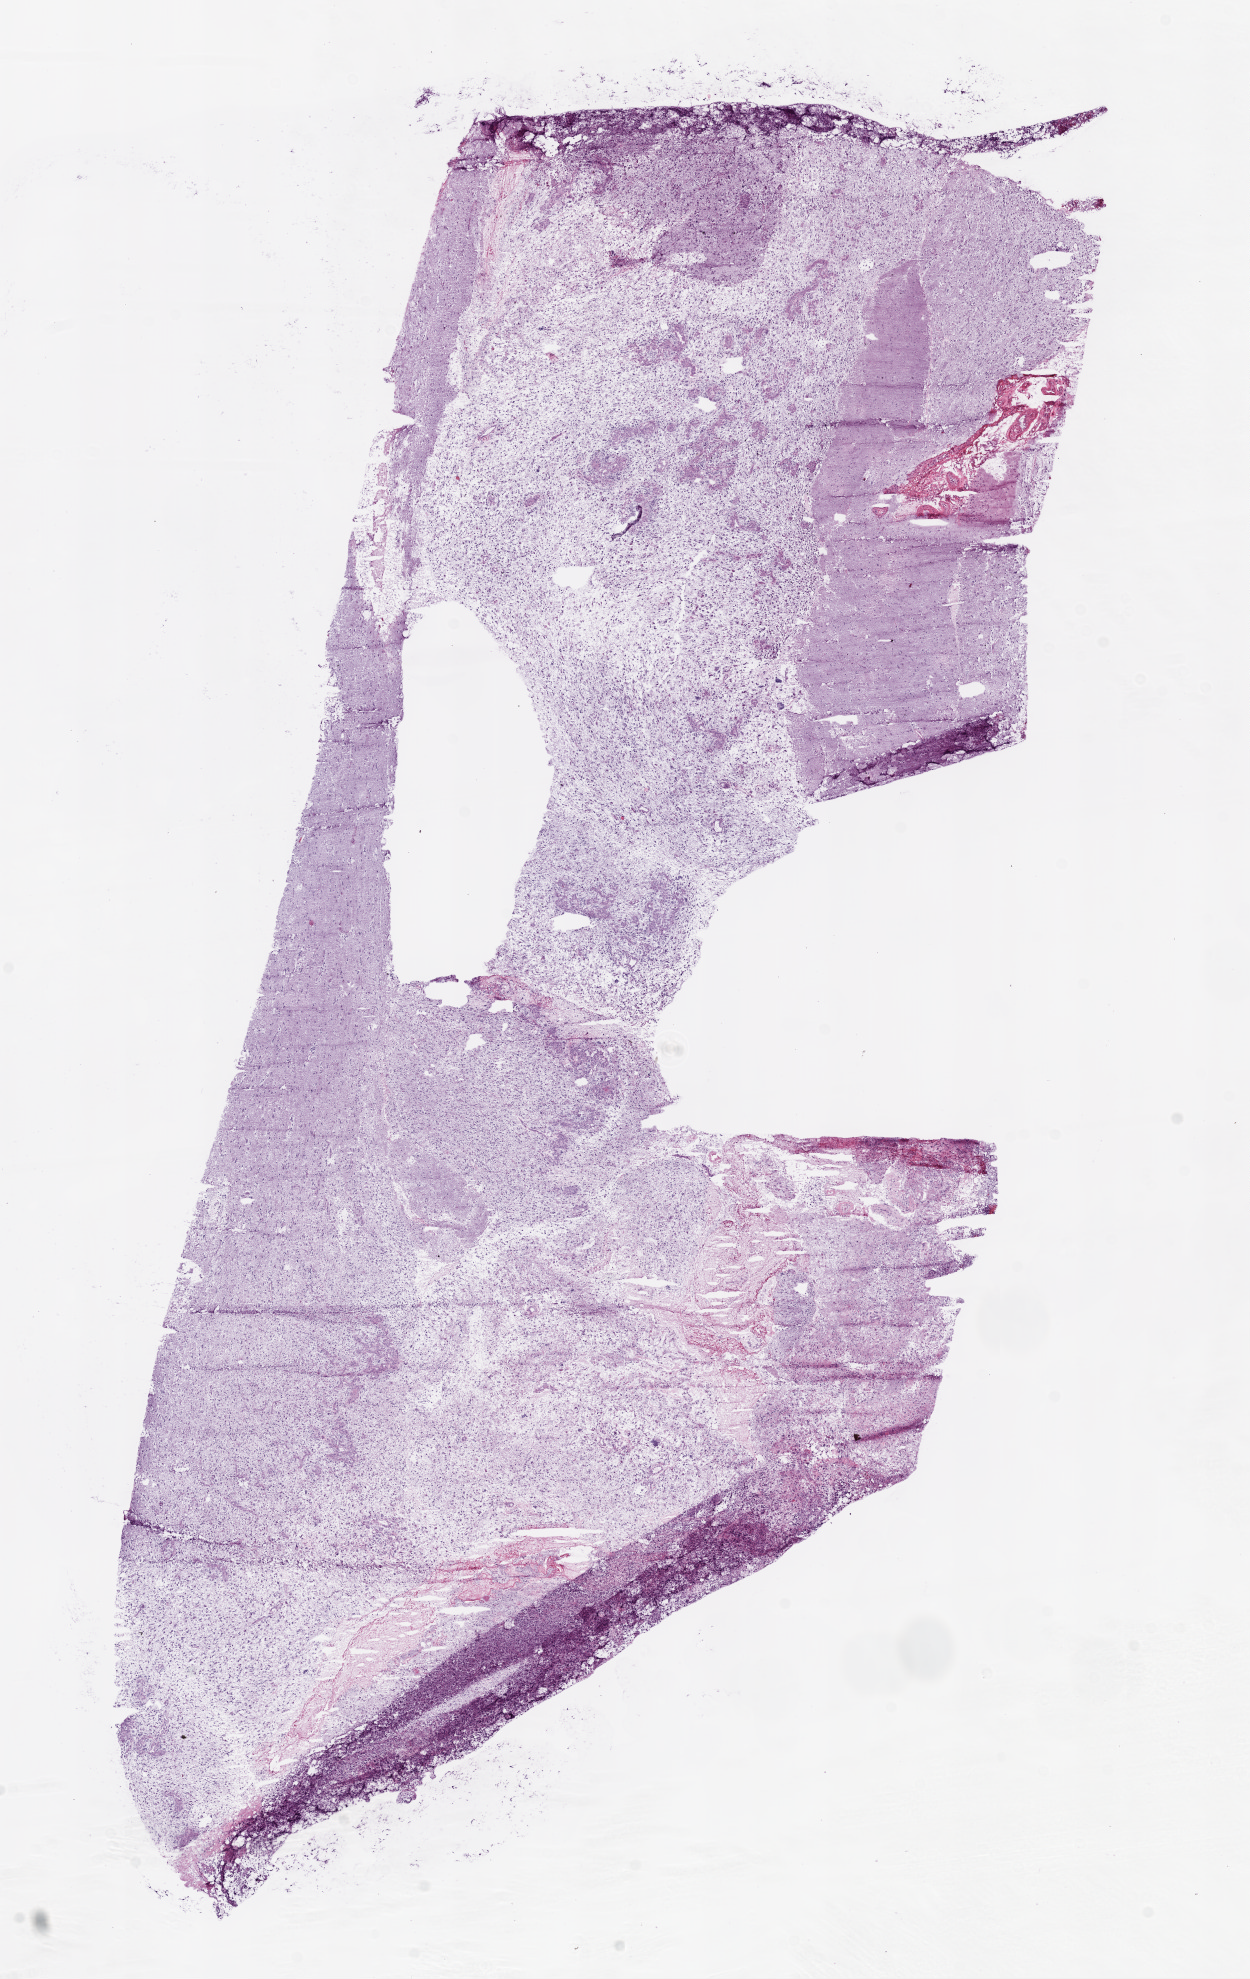
Digitized H&E tissue section (whole slide) — a low-resolution overview of the entire scanned area, about 10.0 x 15.9 mm. Frozen section from the top of the tissue portion. Sample: primary tumour, brain. Female, age 75 years at initial diagnosis. Slide review estimates, as recorded: tumour cells 100%, tumour nuclei 80%, normal cells 0%, stromal cells 0%, necrosis 0%.
Pathologic diagnosis: Glioblastoma.